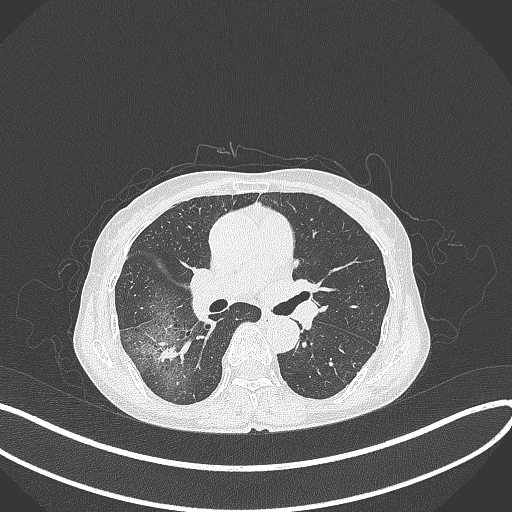
Chest CT, one axial slice. 120 kVp. Lung window (W 1500 / L -600 HU). 1 mm slice thickness. 512 × 512 image matrix. Patient: female, 69 years. Case-level facts recorded for this patient, not image findings: clinical TNM (as recorded): T1b N0 M0.
Structures marked on this image (bounding box drawn by a radiologist):
- lung tumour (recorded histology: adenocarcinoma): box from (x=153, y=334) to (x=198, y=371) px